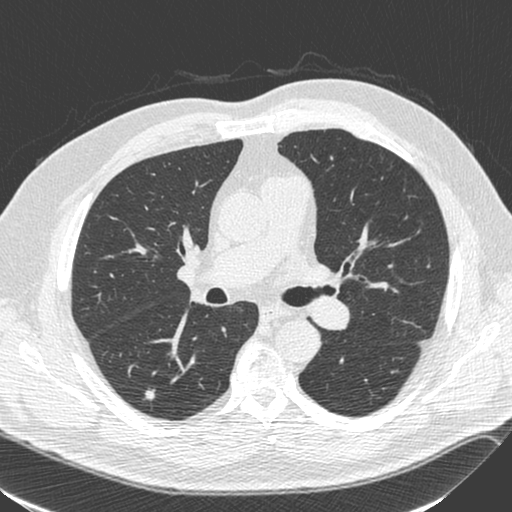
Axial slice from a low-dose chest CT screening exam. Baseline screening round. Lung window (W 1500 / L -600 HU). 1.3 mm slice thickness. 120 kVp. Male participant, aged 71 years at enrolment. Former smoker at enrolment.
Expert reader's lesion annotation, bounding box <137,381,169,408> (left, top, right, bottom; pixels). Reader record for this screening exam (exam-level; its link to the box is not recorded): non-calcified nodule or mass ≥4 mm, right lower lobe, 6 × 6 mm, smooth margins, soft tissue attenuation. Lung cancer was diagnosed 231 days after this screen: squamous cell carcinoma, NOS, right lower lobe, poorly differentiated (G3), stage IA (AJCC 6th edition), 4 mm at pathology.